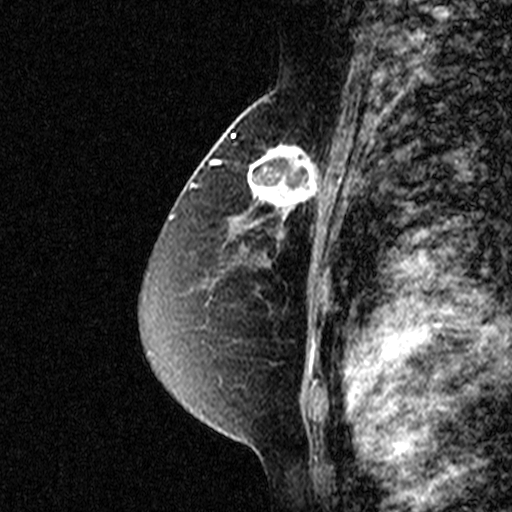
Breast MRI (dynamic contrast-enhanced), one sagittal slice; slice 27 of 44 in the series (ordered by position); dynamic contrast-enhanced study with each time point stored as its own series, time point 2 of 3 at this slice position (early post-contrast, ordered by acquisition time); 1.5 T; TE 4.5 ms, TR 11 ms; 512 × 512 image matrix, field of view 200 × 200 mm. Patient: female, 49 years. Case-level facts recorded for this patient, not image findings: setting: breast cancer imaged before/during neoadjuvant chemotherapy; receptor status: triple-negative.
Structures marked on this image (semi-automatically segmented with operator editing):
- analysis volume of interest (the breast-tissue region the enhancement analysis was run in; not a lesion): box from (x=238, y=122) to (x=331, y=227) px
- tumour enhancement mask (voxels above the 90 % enhancement threshold inside the analysis volume of interest): (x=249, y=144)–(x=318, y=219)